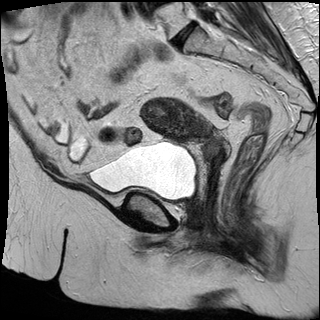
Pelvic MRI for cervical cancer, one sagittal slice. T2-weighted. 1.5 T. TE 87 ms, TR 3063.4 ms. 320 × 320 image matrix. Patient: female, 53 years.
Structures marked on this image (manually delineated by an expert):
- uterus and cervix: bounding box [x1, y1, x2, y2] px = [140, 97, 225, 167]